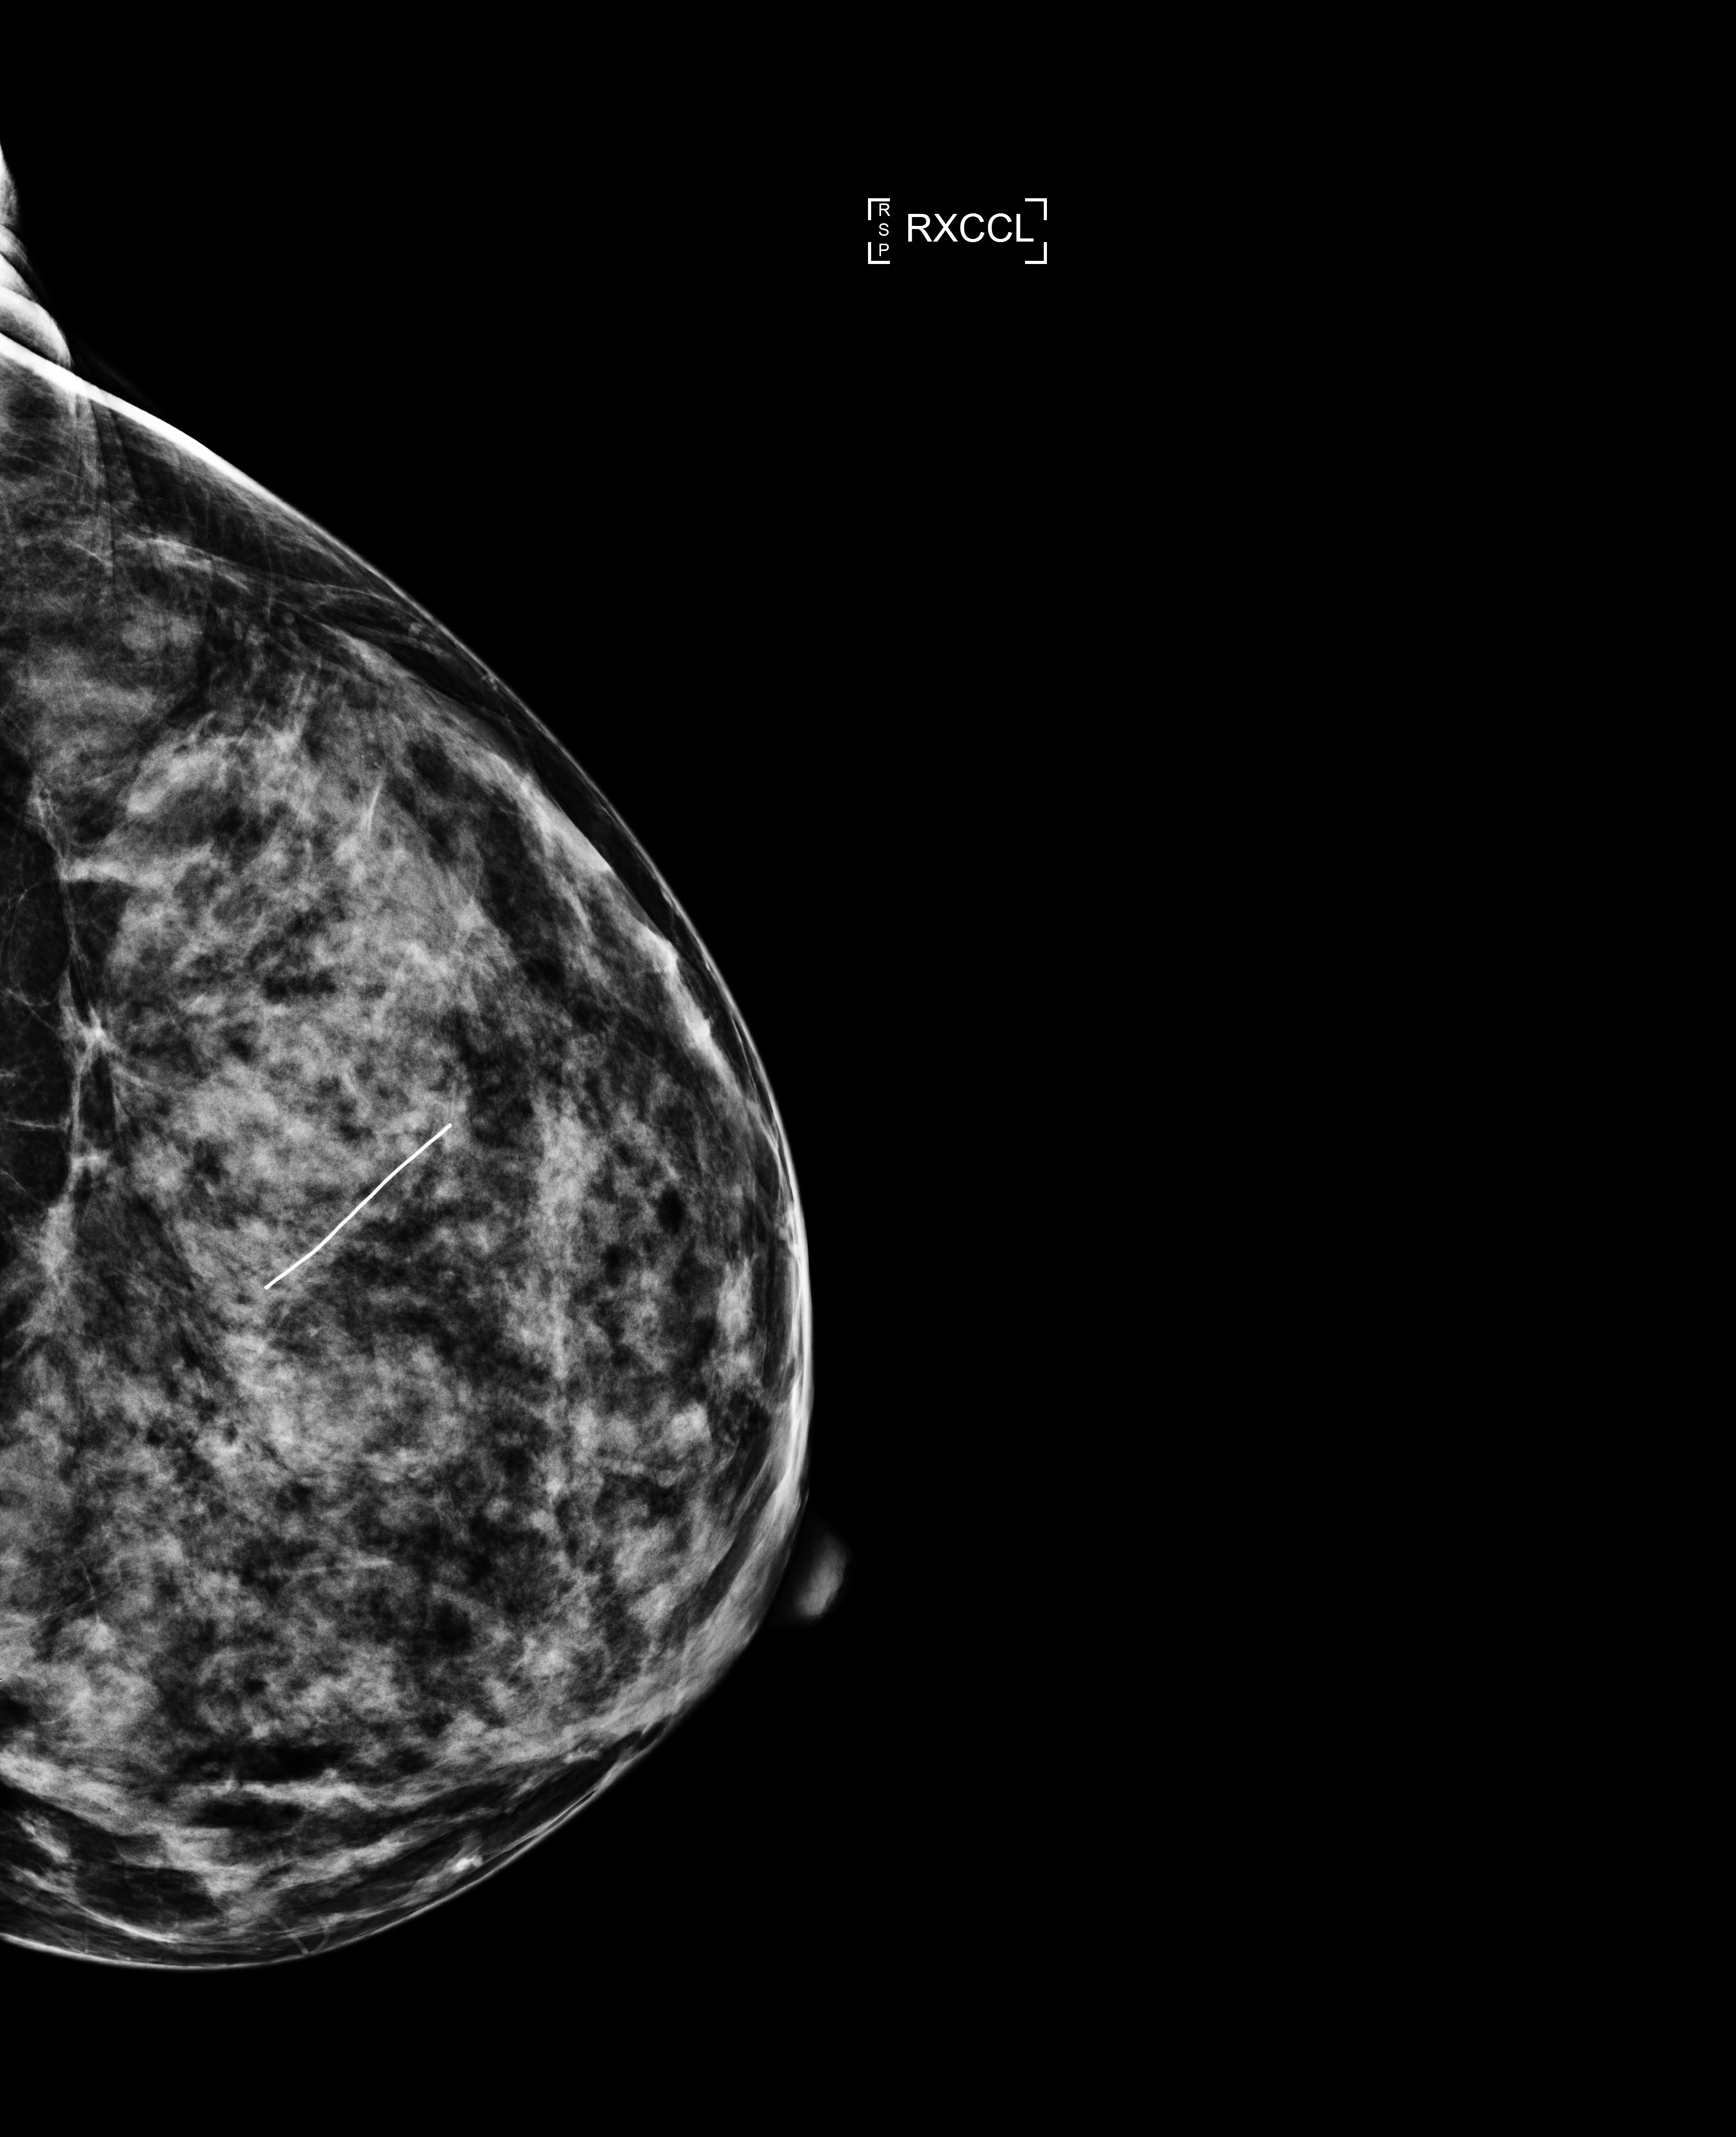
Full-field digital mammogram (FFDM), right breast, laterally exaggerated craniocaudal (XCCL) view, annual screening mammography examination, compressed breast thickness 59 mm. Female patient, age 51 years.
BI-RADS breast density category at the screening exam (both breasts, scale 1–4): 3. Final BI-RADS category for the screening round (tomosynthesis exam, both breasts): category 2. Recall: no recall after this screen.